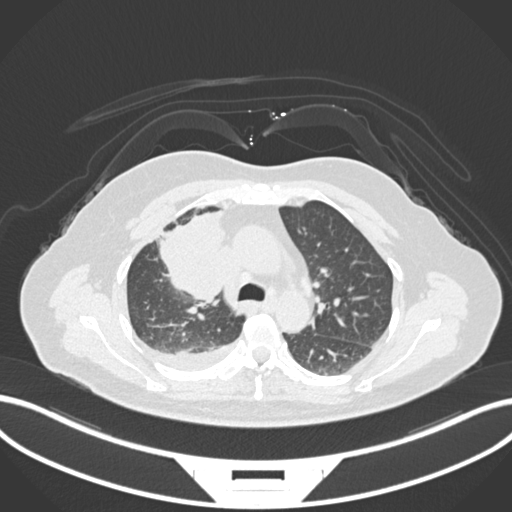
Chest CT, one axial slice; slice 105 of 172 in the series (ordered by position); 120 kVp; lung window (W 1500 / L -600 HU); 1 mm slice thickness; 512 × 512 image matrix. Female patient, age 52 years. From the clinical record (not read from this slice): clinical TNM (as recorded): T3 N1 M1.
Outlined on this slice (rectangle marked by the reading radiologist):
- lung tumour (recorded histology: adenocarcinoma): box from (x=153, y=207) to (x=236, y=305) px